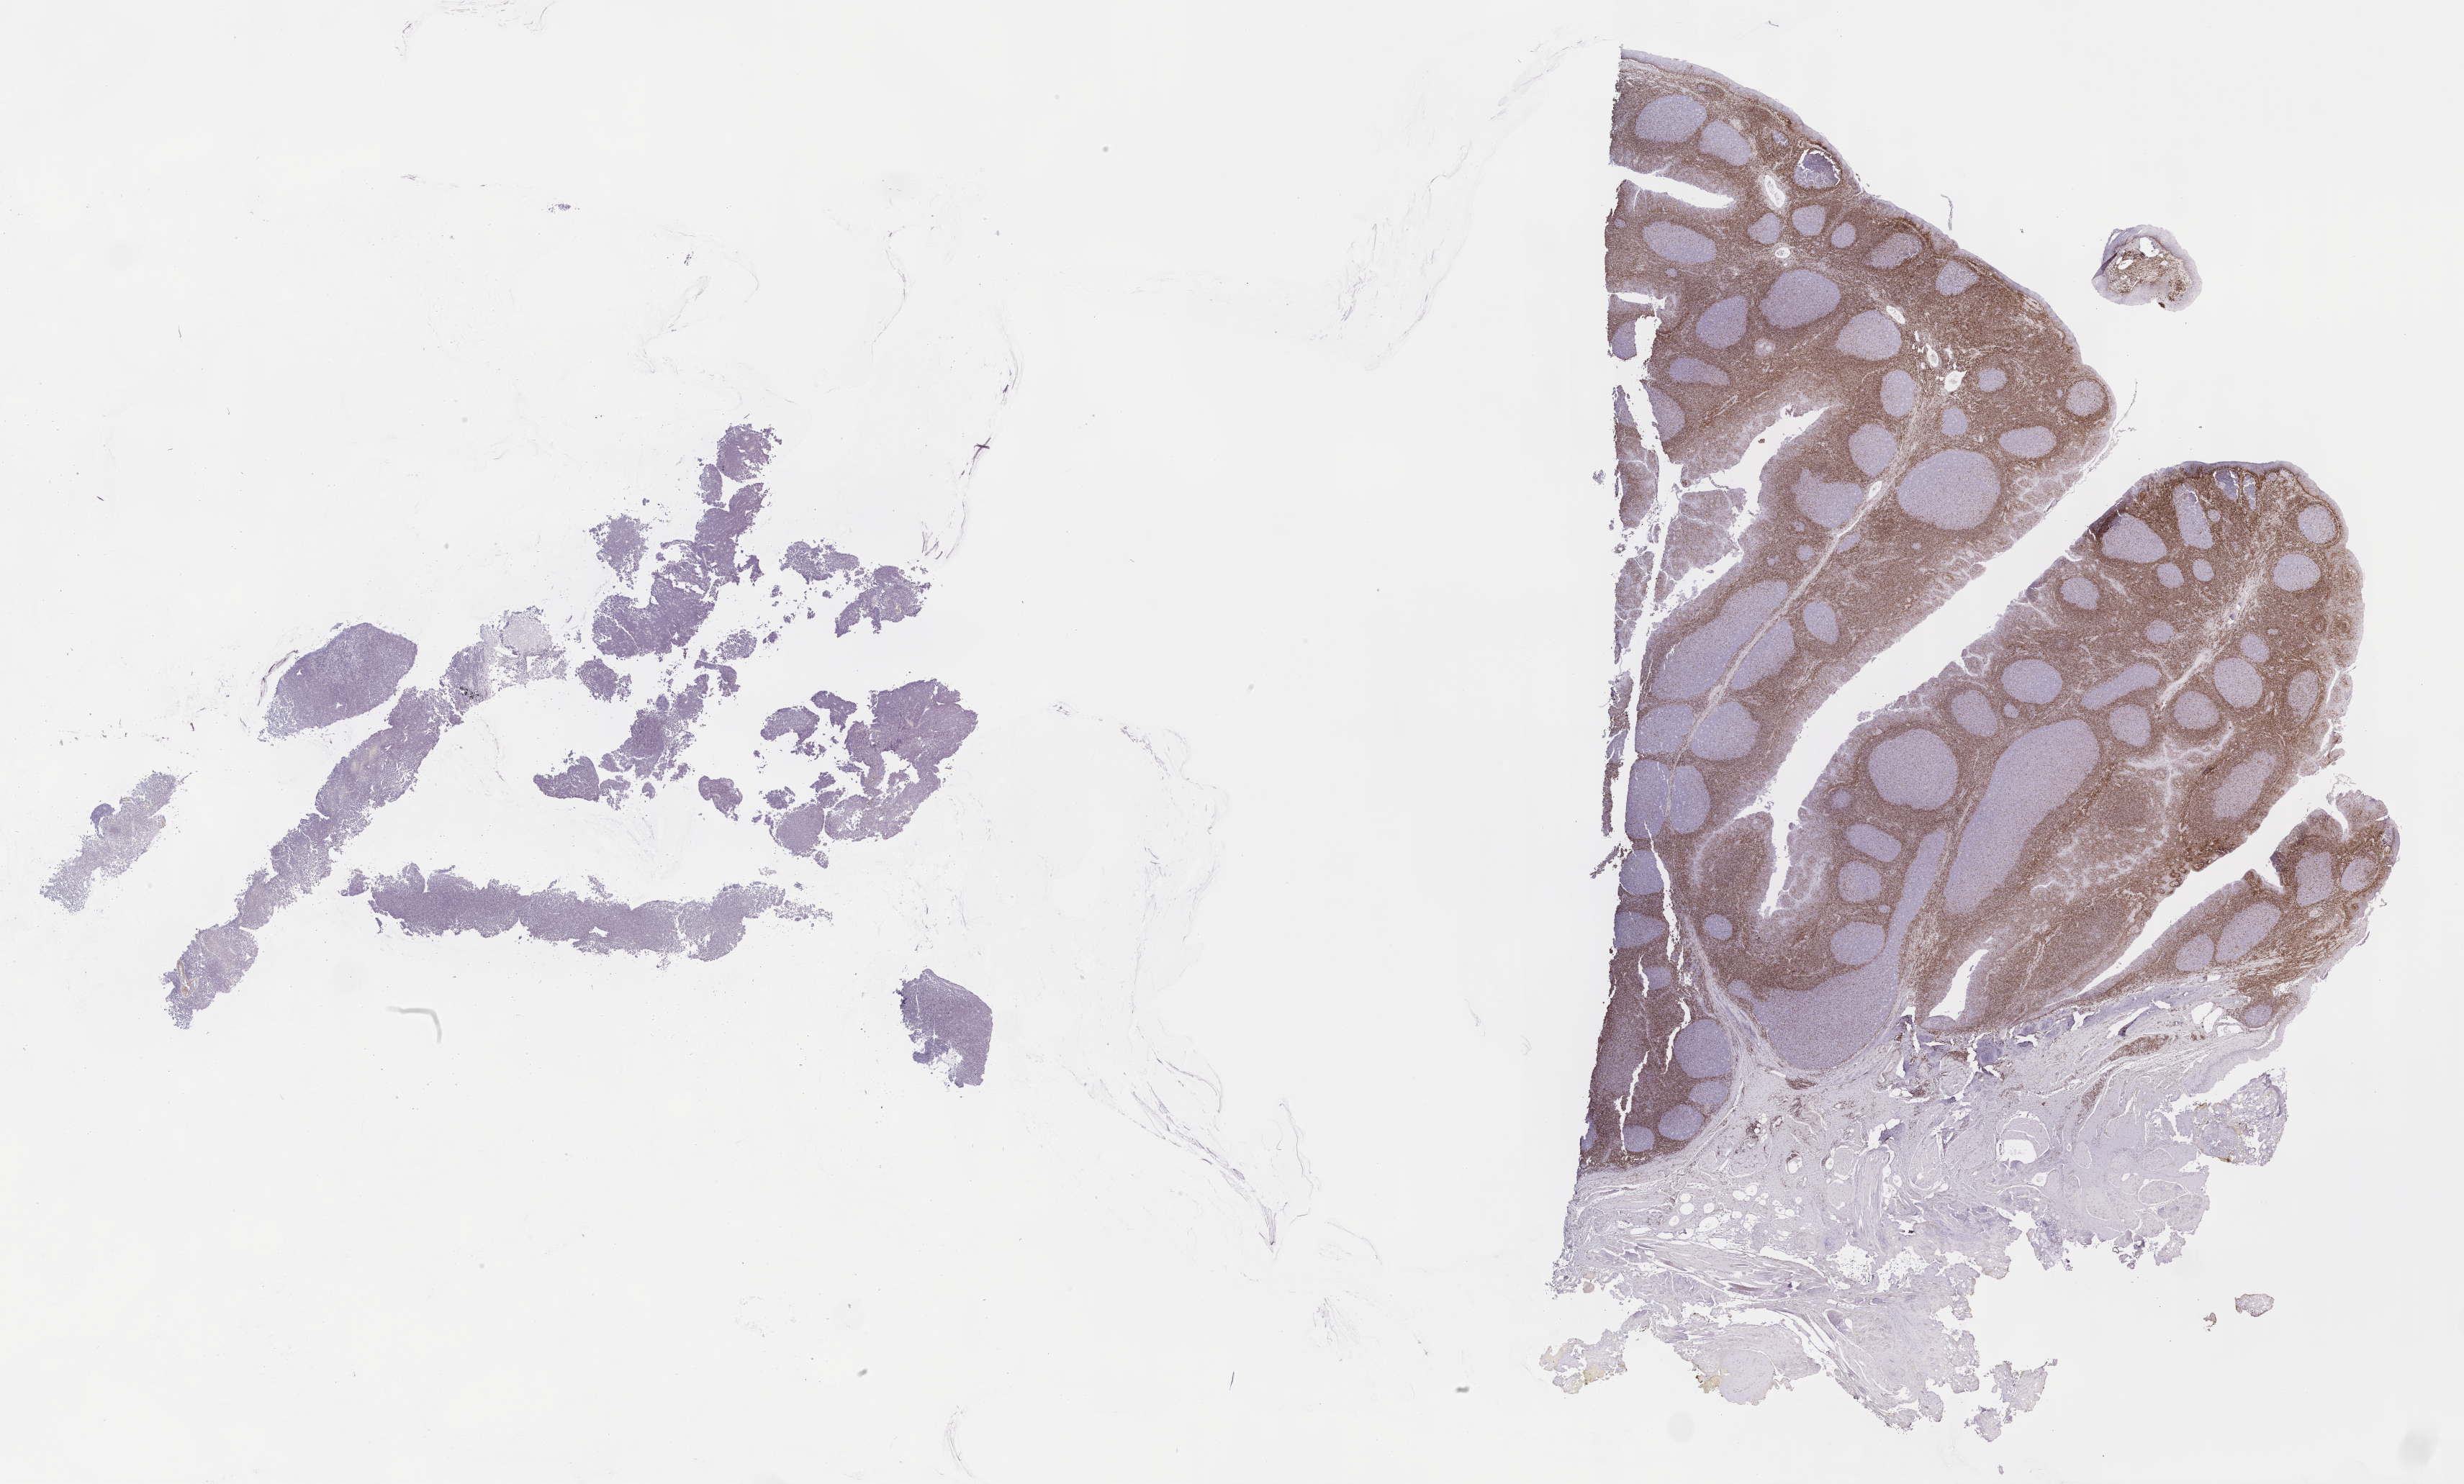
IHC for BCL2, whole-slide image, a low-resolution overview of the entire scanned area, about 27.7 x 16.7 mm; tumor tissue; anatomic site: kidney. Male patient; age at initial diagnosis 3 years.
Histologic diagnosis: Burkitt lymphoma, NOS.